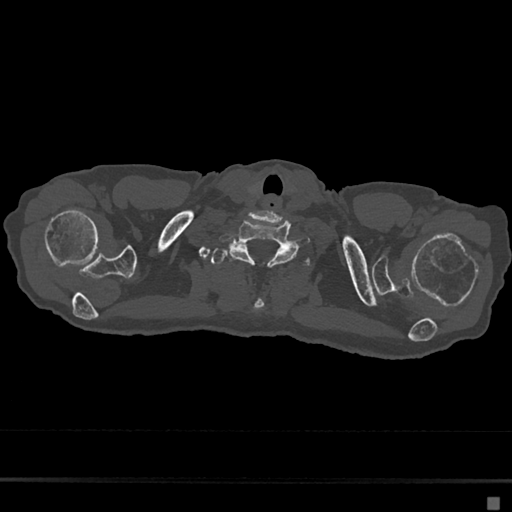
CT including the spine, one axial slice; reconstruction kernel Br40s/3; bone window (W 1800 / L 400 HU); 0.5 mm slice thickness; 512 × 512 image matrix, field of view 360 × 360 mm. Patient: female, 68 years. From the clinical record (not read from this slice): primary cancer: renal.
Structures marked on this image (semi-automatic segmentation, software-assisted and operator-edited):
- T1 vertebra: bounding box [x1, y1, x2, y2] px = [210, 243, 310, 311]